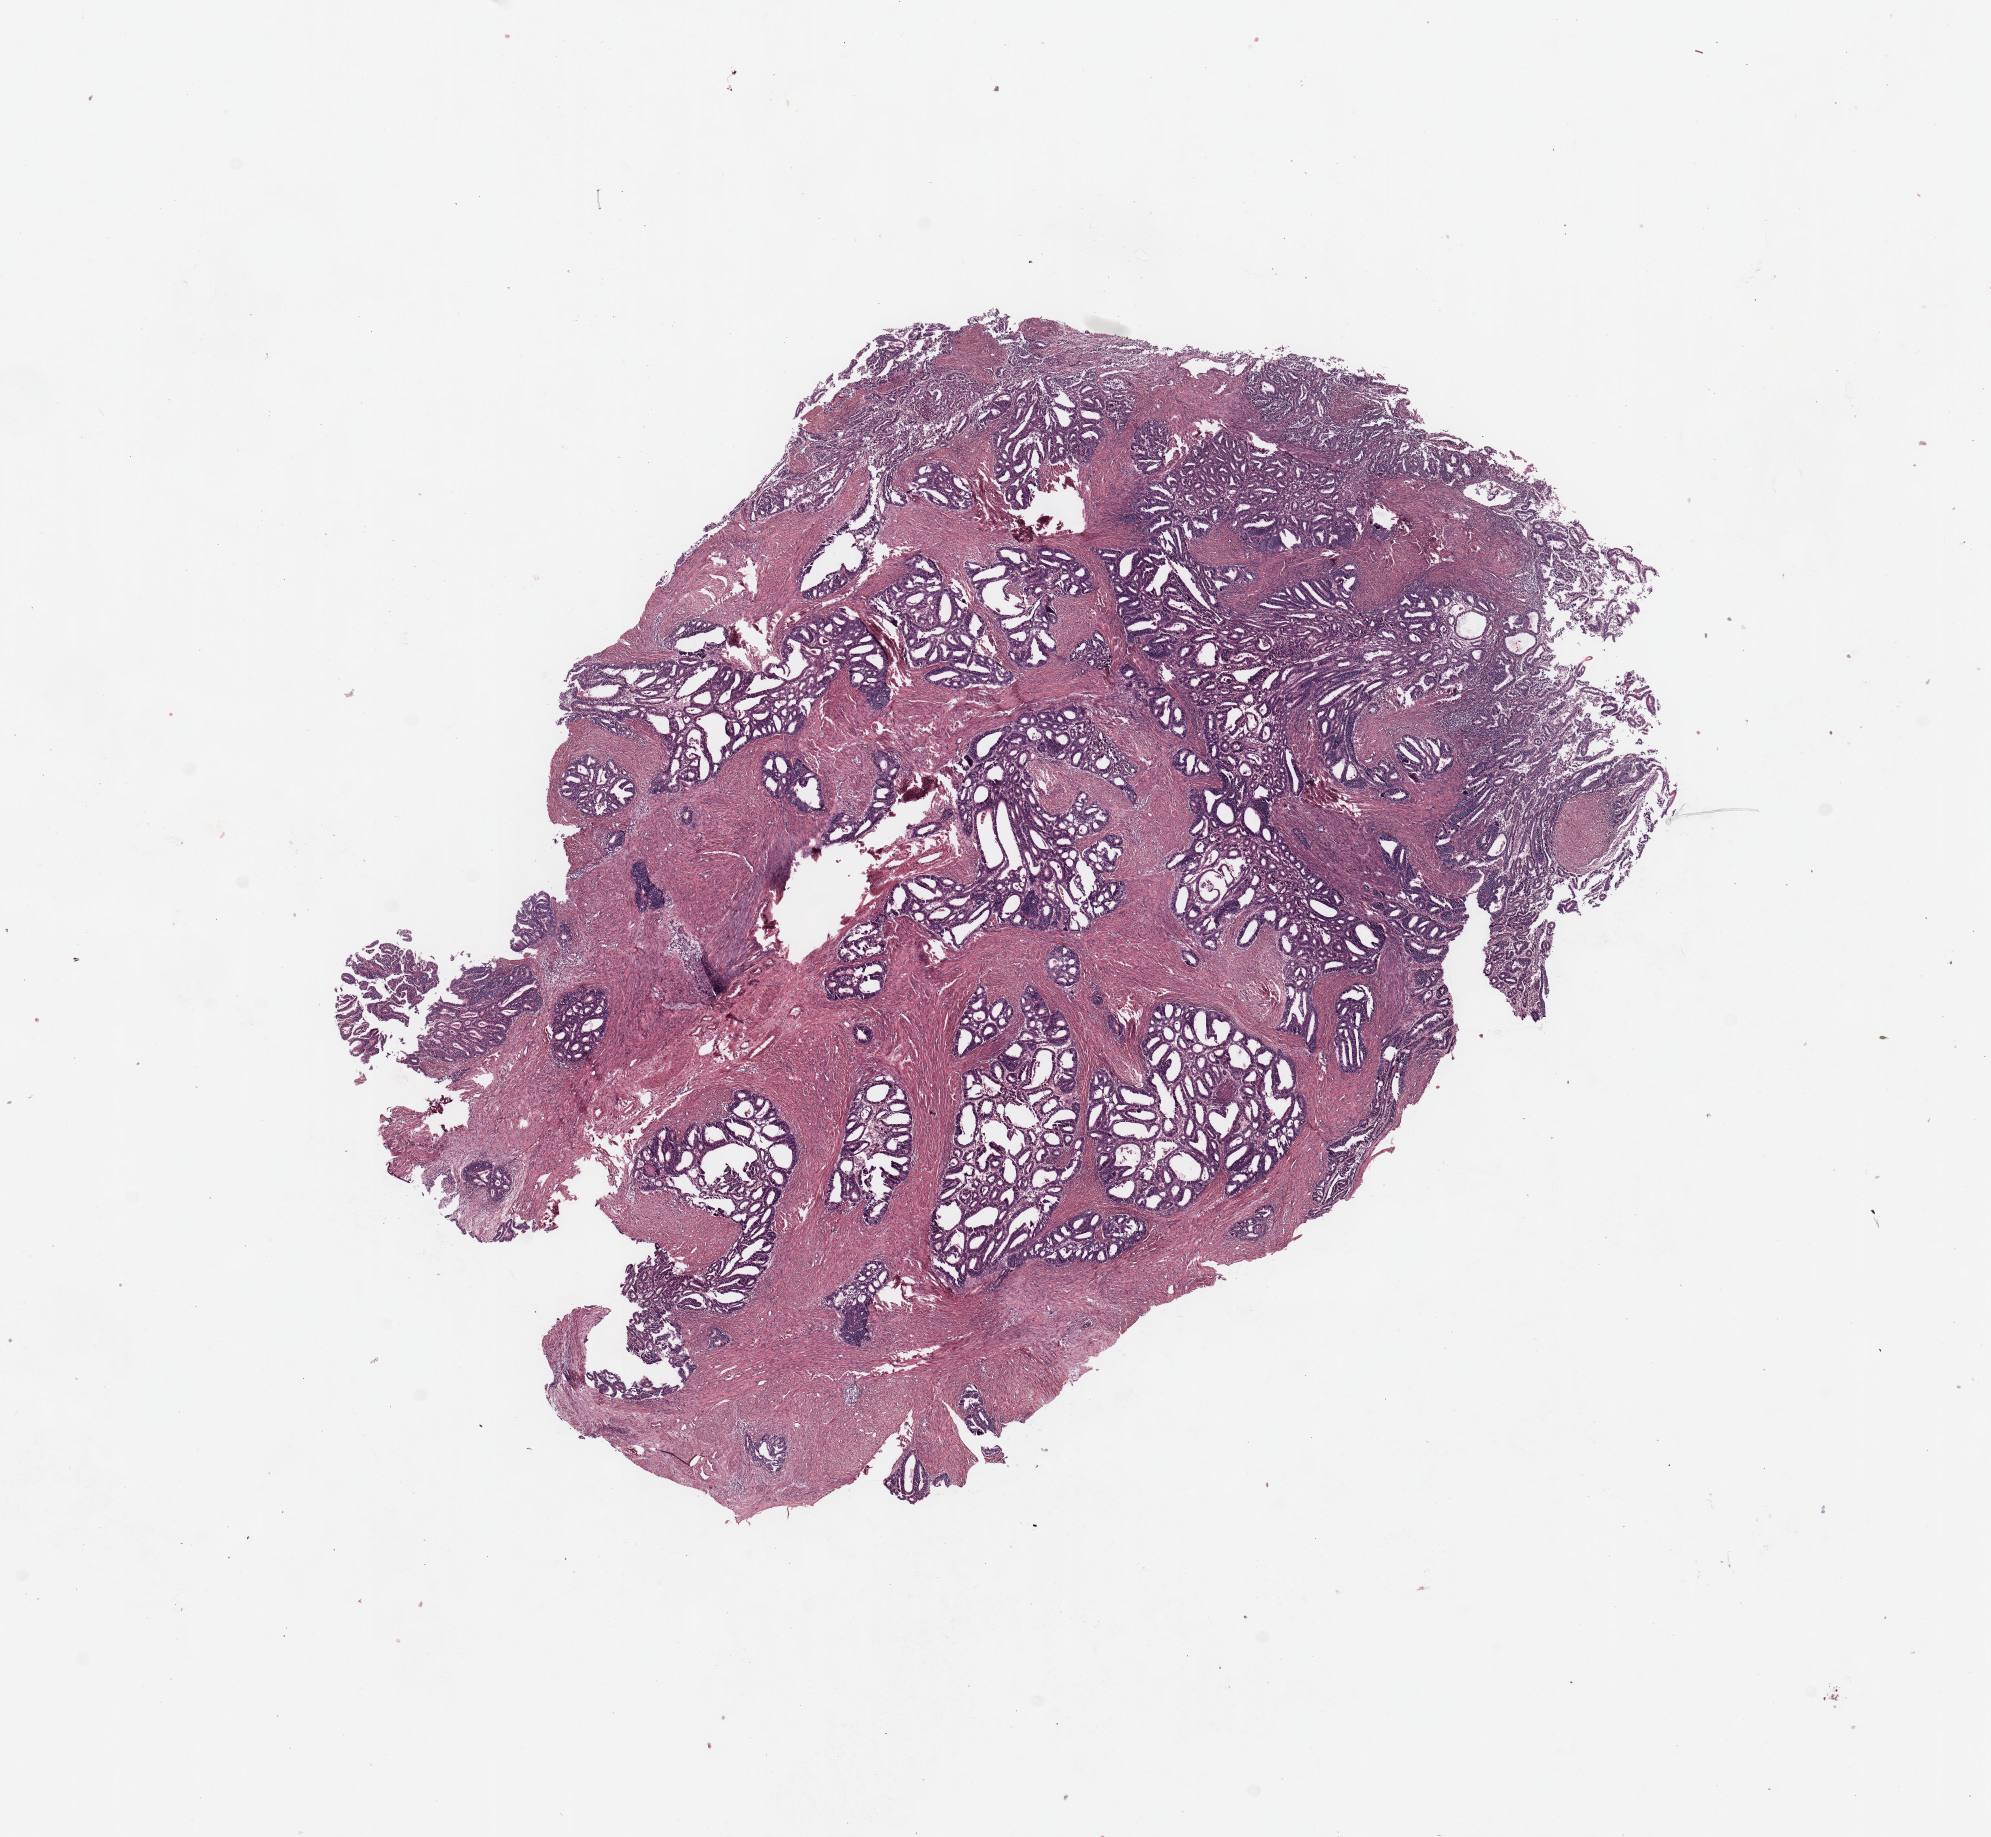
H&E-stained whole-slide image — low-resolution overview of the scanned area, about 15.8 x 14.5 mm. Uterus, tumour tissue. 67-year-old female patient. Histologic grade: G2 (moderately differentiated).
* diagnosis: Endometrioid adenocarcinoma, NOS
* AJCC pathologic stage: I